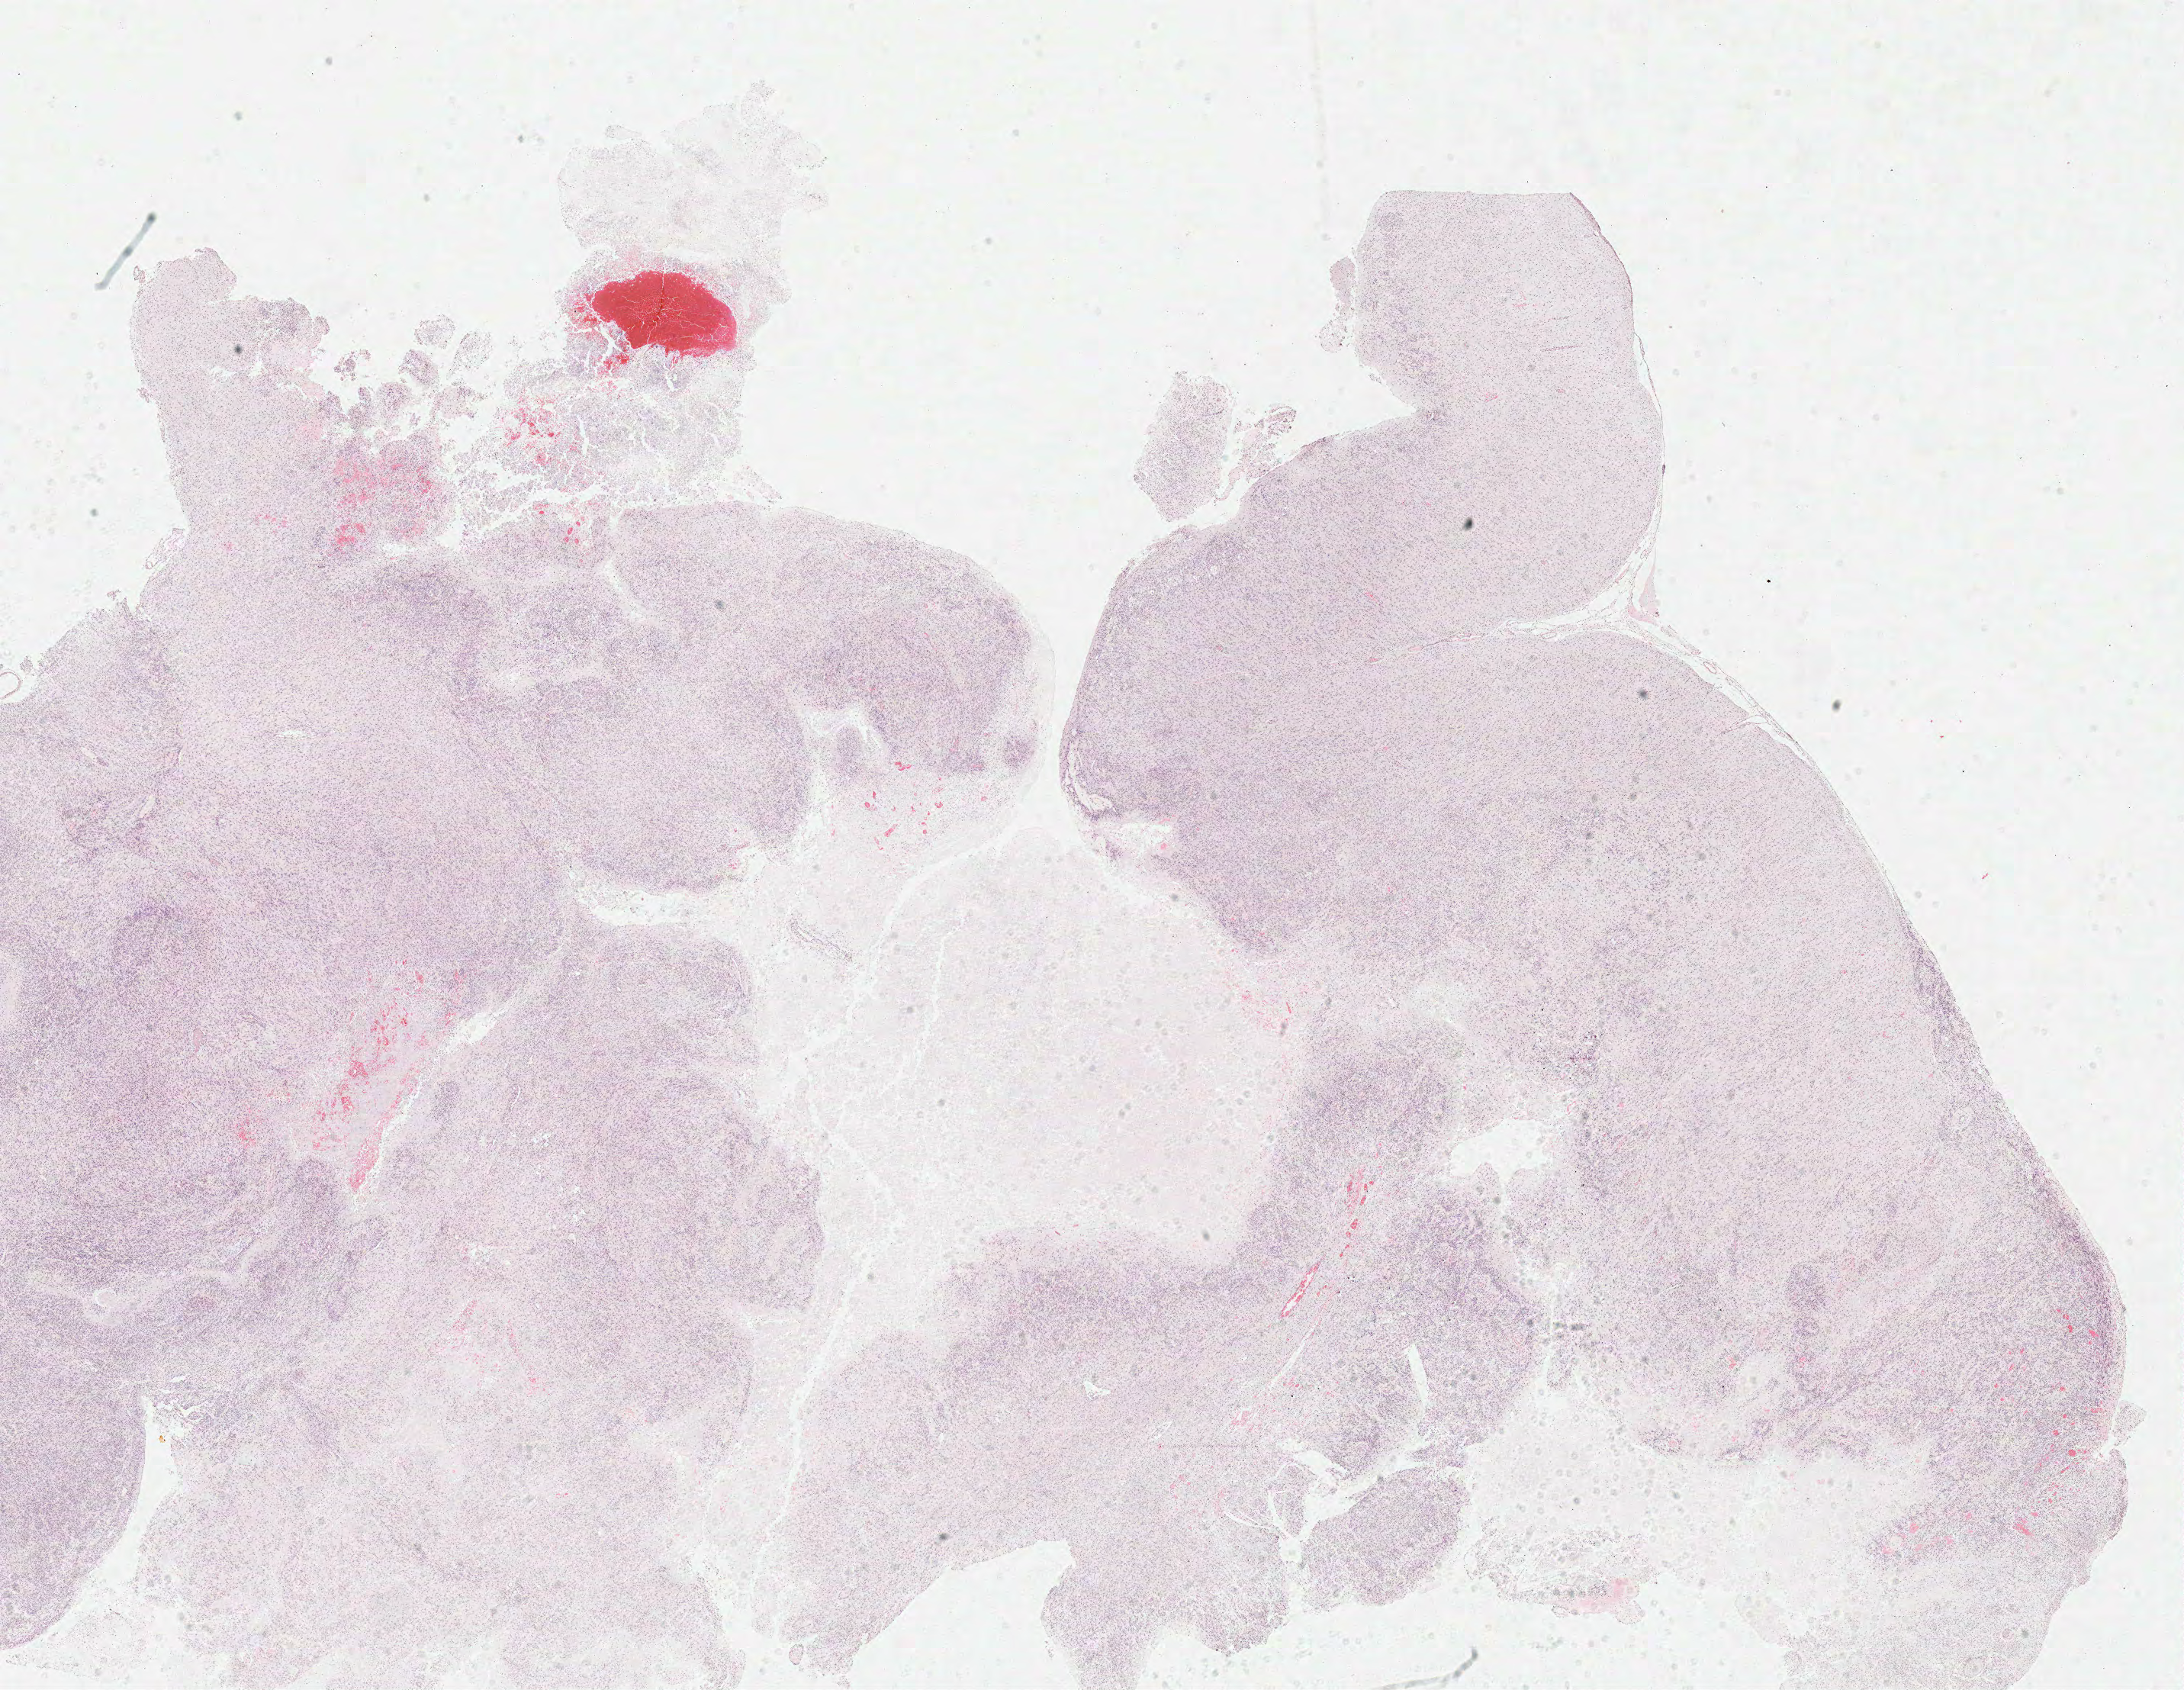
Whole-slide histology image, Hematoxylin and eosin (H&E) stained, shown as a low-resolution overview of the whole scanned area (about 22.5 x 17.4 mm, from a 40x scan), formalin-fixed paraffin-embedded (FFPE) diagnostic section, brain, primary tumour sample. Patient: female, age at initial diagnosis 77 years.
• pathologic diagnosis: Glioblastoma